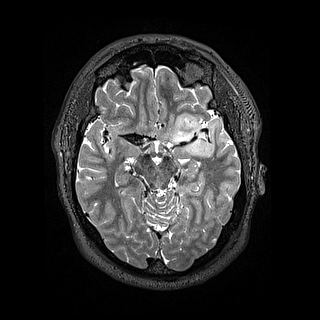
Brain MRI from a brain-tumour surgery series, one axial slice; 1.2 mm slice thickness; 320 × 320 image matrix, field of view 254 × 254 mm. Case-level facts recorded for this patient, not image findings: histopathology: Astrocytoma; WHO grade: 2; IDH mutation: yes.
Annotated regions visible in this slice (manually delineated by an expert):
- tumour: box from (x=171, y=111) to (x=206, y=157) px